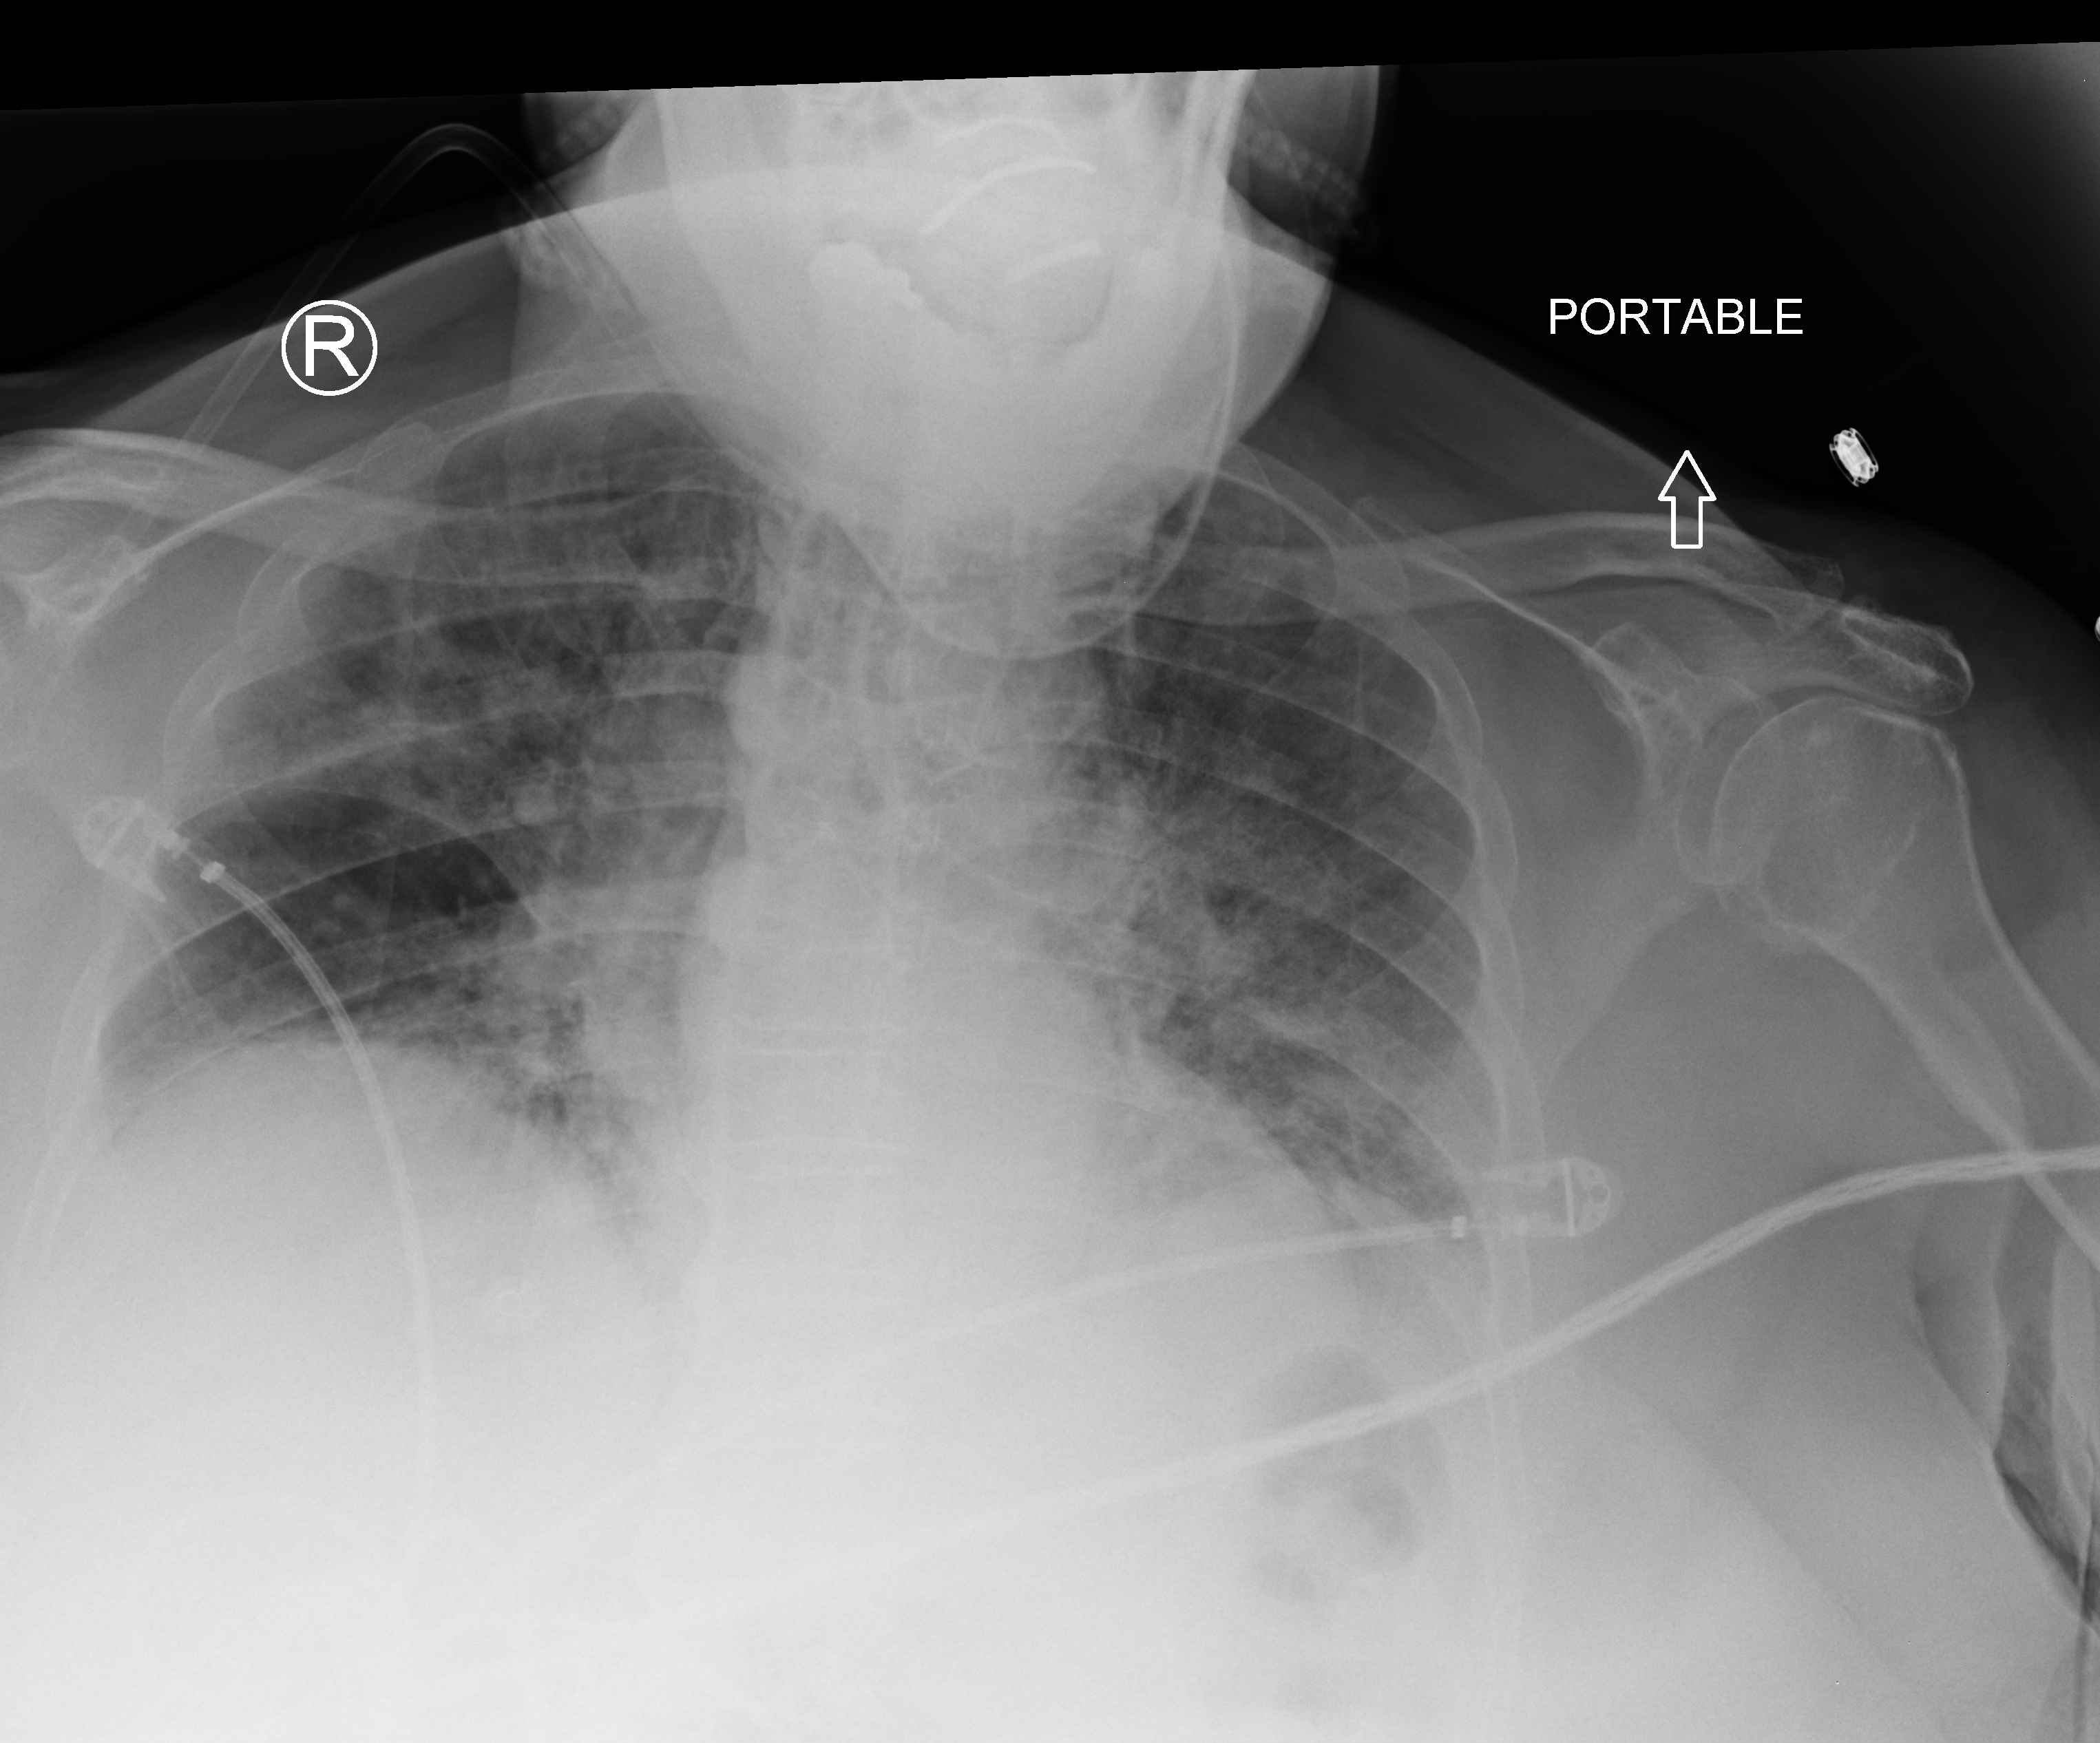
Bedside chest radiograph (computed radiography); anteroposterior (AP) projection. Female patient hospitalised with COVID-19, age 75–90 years.
Admission-level facts for this patient (not findings on this image; timing relative to this image not recorded): COPD (admission record): no; smoking status (admission record): never; hypertension (admission record): yes.